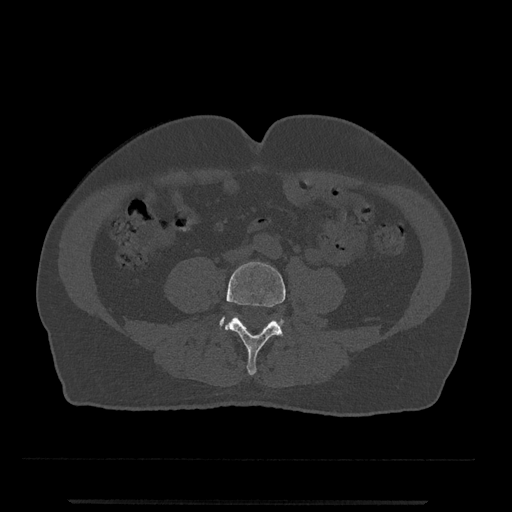
CT including the spine, one axial slice; slice 125 of 797 in the series (ordered by position); reconstruction kernel Br40s/3; bone window (W 1800 / L 400 HU); 0.5 mm slice thickness; 512 × 512 image matrix, field of view 419 × 419 mm. Male patient, age 63 years. From the clinical record (not read from this slice): primary cancer: prostate.
Annotated regions visible in this slice (semi-automatic segmentation, software-assisted and operator-edited):
- L4 vertebra: box from (x=225, y=262) to (x=286, y=375) px
- L5 vertebra: (x=220, y=317)–(x=282, y=328)